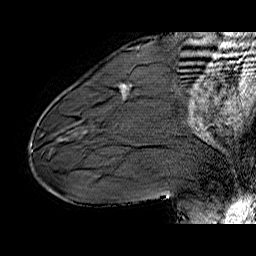
Breast MRI (dynamic contrast-enhanced), one sagittal slice. Dynamic contrast-enhanced series, time point 2 of 6 at this slice position (early post-contrast). 1.5 T. TE 6.4 ms, TR 32.9 ms. 4 mm slice thickness. 256 × 256 image matrix, field of view 200 × 200 mm. Female patient. Case-level facts recorded for this patient, not image findings: setting: breast cancer imaged before/during neoadjuvant chemotherapy; receptor status: HER2-positive.
Outlined on this slice (semi-automatically segmented with operator editing):
- analysis volume of interest (the breast-tissue region the enhancement analysis was run in; not a lesion): bounding box (x1, y1, x2, y2) in pixels: (120, 85, 126, 92)
- tumour enhancement mask (voxels above the 100 % enhancement threshold inside the analysis volume of interest): (123, 85, 125, 87)